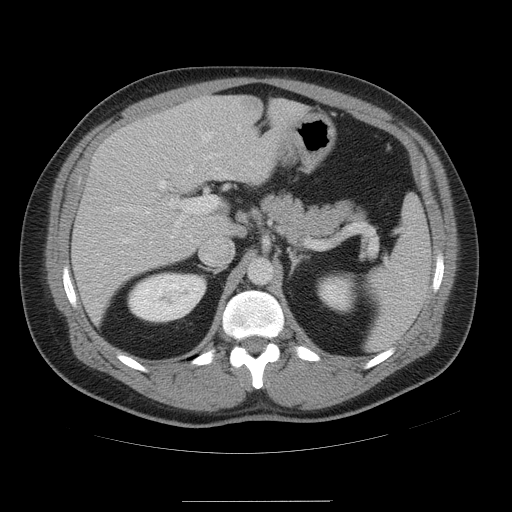
Contrast-enhanced abdominal CT, one axial slice; position 31 of 54 along the scan axis; 120 kVp; intravenous contrast given; soft-tissue window (W 400 / L 40 HU); 5 mm slice thickness; 512 × 512 image matrix. Male patient, age 40 years. From the clinical record (not read from this slice): diagnosis: colorectal cancer liver metastases, imaged before liver resection; multiple liver metastases: no; largest metastasis: 15 cm; chemotherapy before resection: no.
Annotated regions visible in this slice (manually delineated by an expert):
- hepatic veins: bounding box <149,128,219,244> (left, top, right, bottom; pixels)
- liver: <71,96,307,325>
- planned liver remnant (the part of the liver to remain after resection): <201,95,307,235>
- portal vein (with intrahepatic branches): <129,180,218,238>